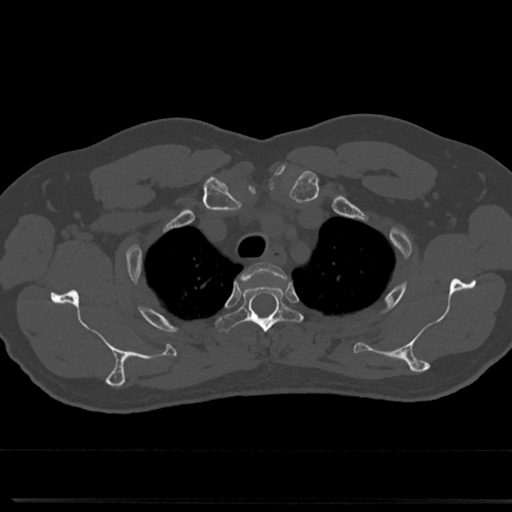
CT including the spine, one axial slice; slice 601 of 817 in the series (ordered by position); reconstruction kernel Br40s/3; 120 kVp; bone window (W 1800 / L 400 HU); 0.5 mm slice thickness; 512 × 512 image matrix, field of view 355 × 355 mm. Patient: male, 61 years. Case-level facts recorded for this patient, not image findings: primary cancer: prostate.
Structures marked on this image (semi-automatically segmented with operator editing):
- T2 vertebra: bounding box (x1, y1, x2, y2) in pixels: (247, 263, 282, 276)
- T3 vertebra: (221, 275, 296, 341)